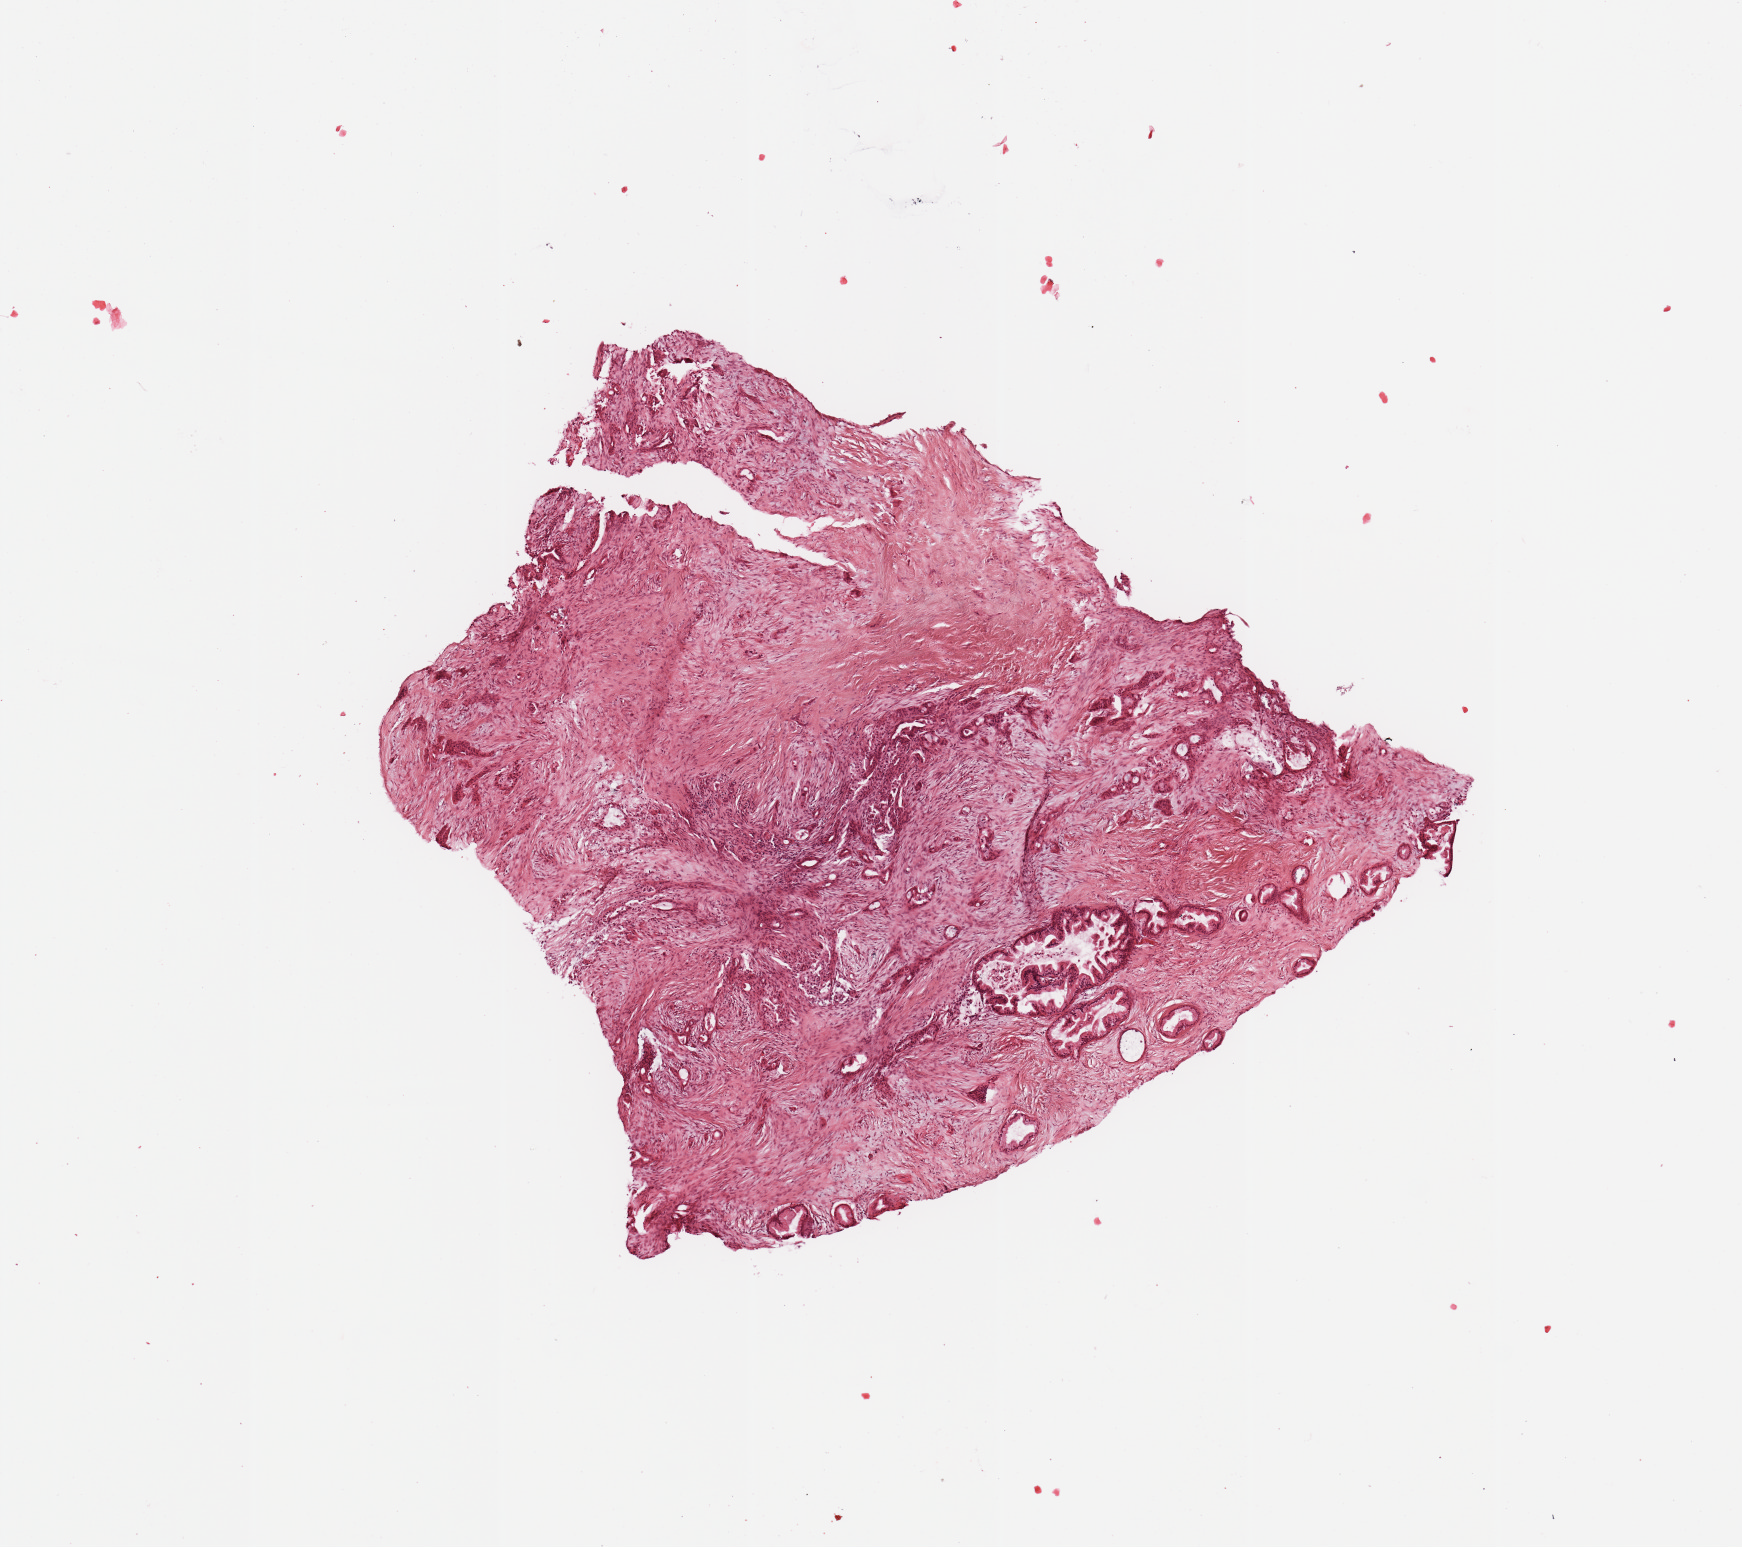
Whole-slide histology image, Hematoxylin and eosin (H&E) stained, low-resolution overview of the scanned area, about 6.9 x 6.1 mm (acquisition: 20x scan). Pancreas, tumour tissue. Male, 69 y/o. Histologic grade: G3 (poorly differentiated).
* histologic diagnosis: Infiltrating duct carcinoma, NOS
* primary tumour site (as recorded): head
* AJCC pathologic stage: IIB